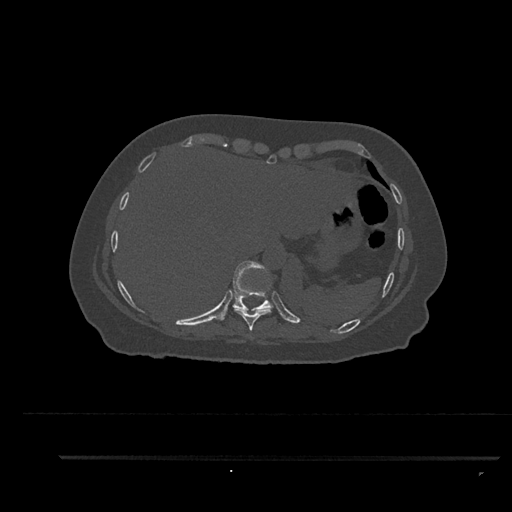
CT including the spine, one axial slice. Position 392 of 797 along the scan axis. Reconstruction kernel Br40s/3. Bone window (W 1800 / L 400 HU). 0.5 mm slice thickness. 512 × 512 image matrix. Female patient, age 44 years. Case-level facts recorded for this patient, not image findings: primary cancer: renal; vertebrae with lytic lesions (as recorded): L1.
Structures marked on this image (semi-automatically segmented with operator editing):
- T10 vertebra: box from (x=220, y=260) to (x=274, y=320) px
- T9 vertebra: (x=235, y=308)–(x=273, y=331)